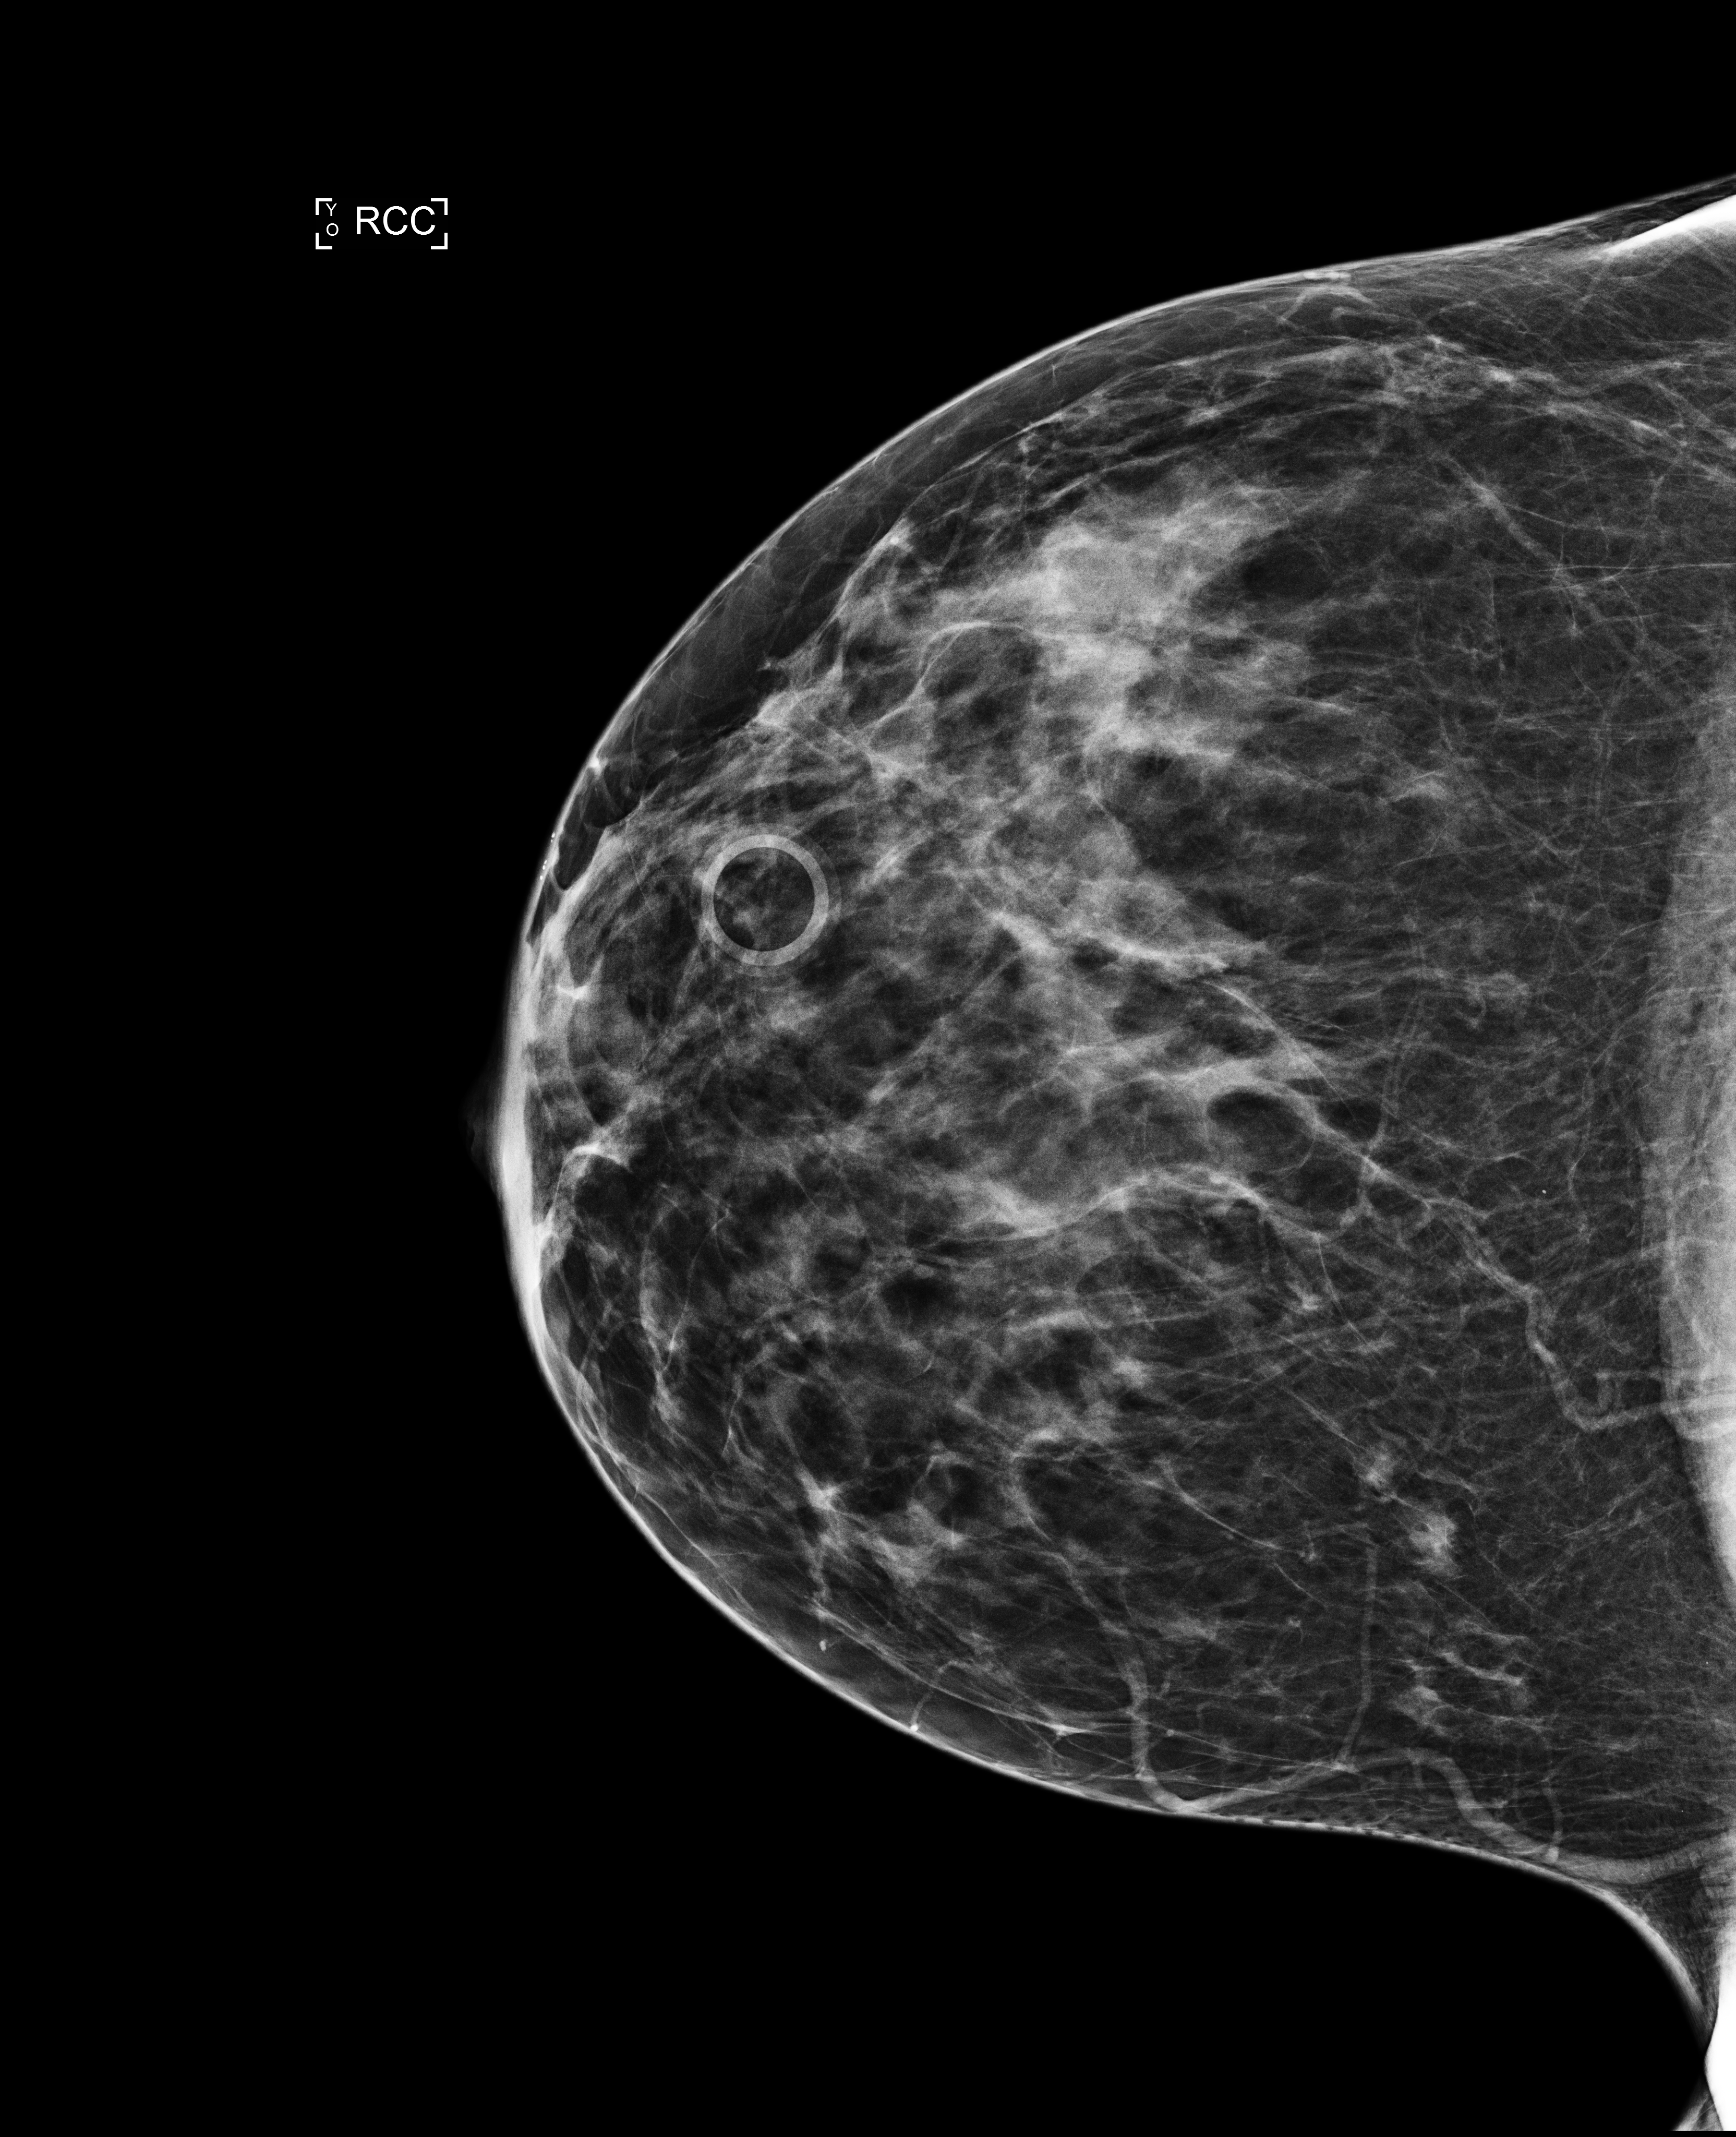
Digital mammogram (FFDM); right breast; cranio-caudal projection; annual screening mammography examination. Female patient, age 46 years.
Final BI-RADS category for the screening round (tomosynthesis exam, both breasts): category 2.